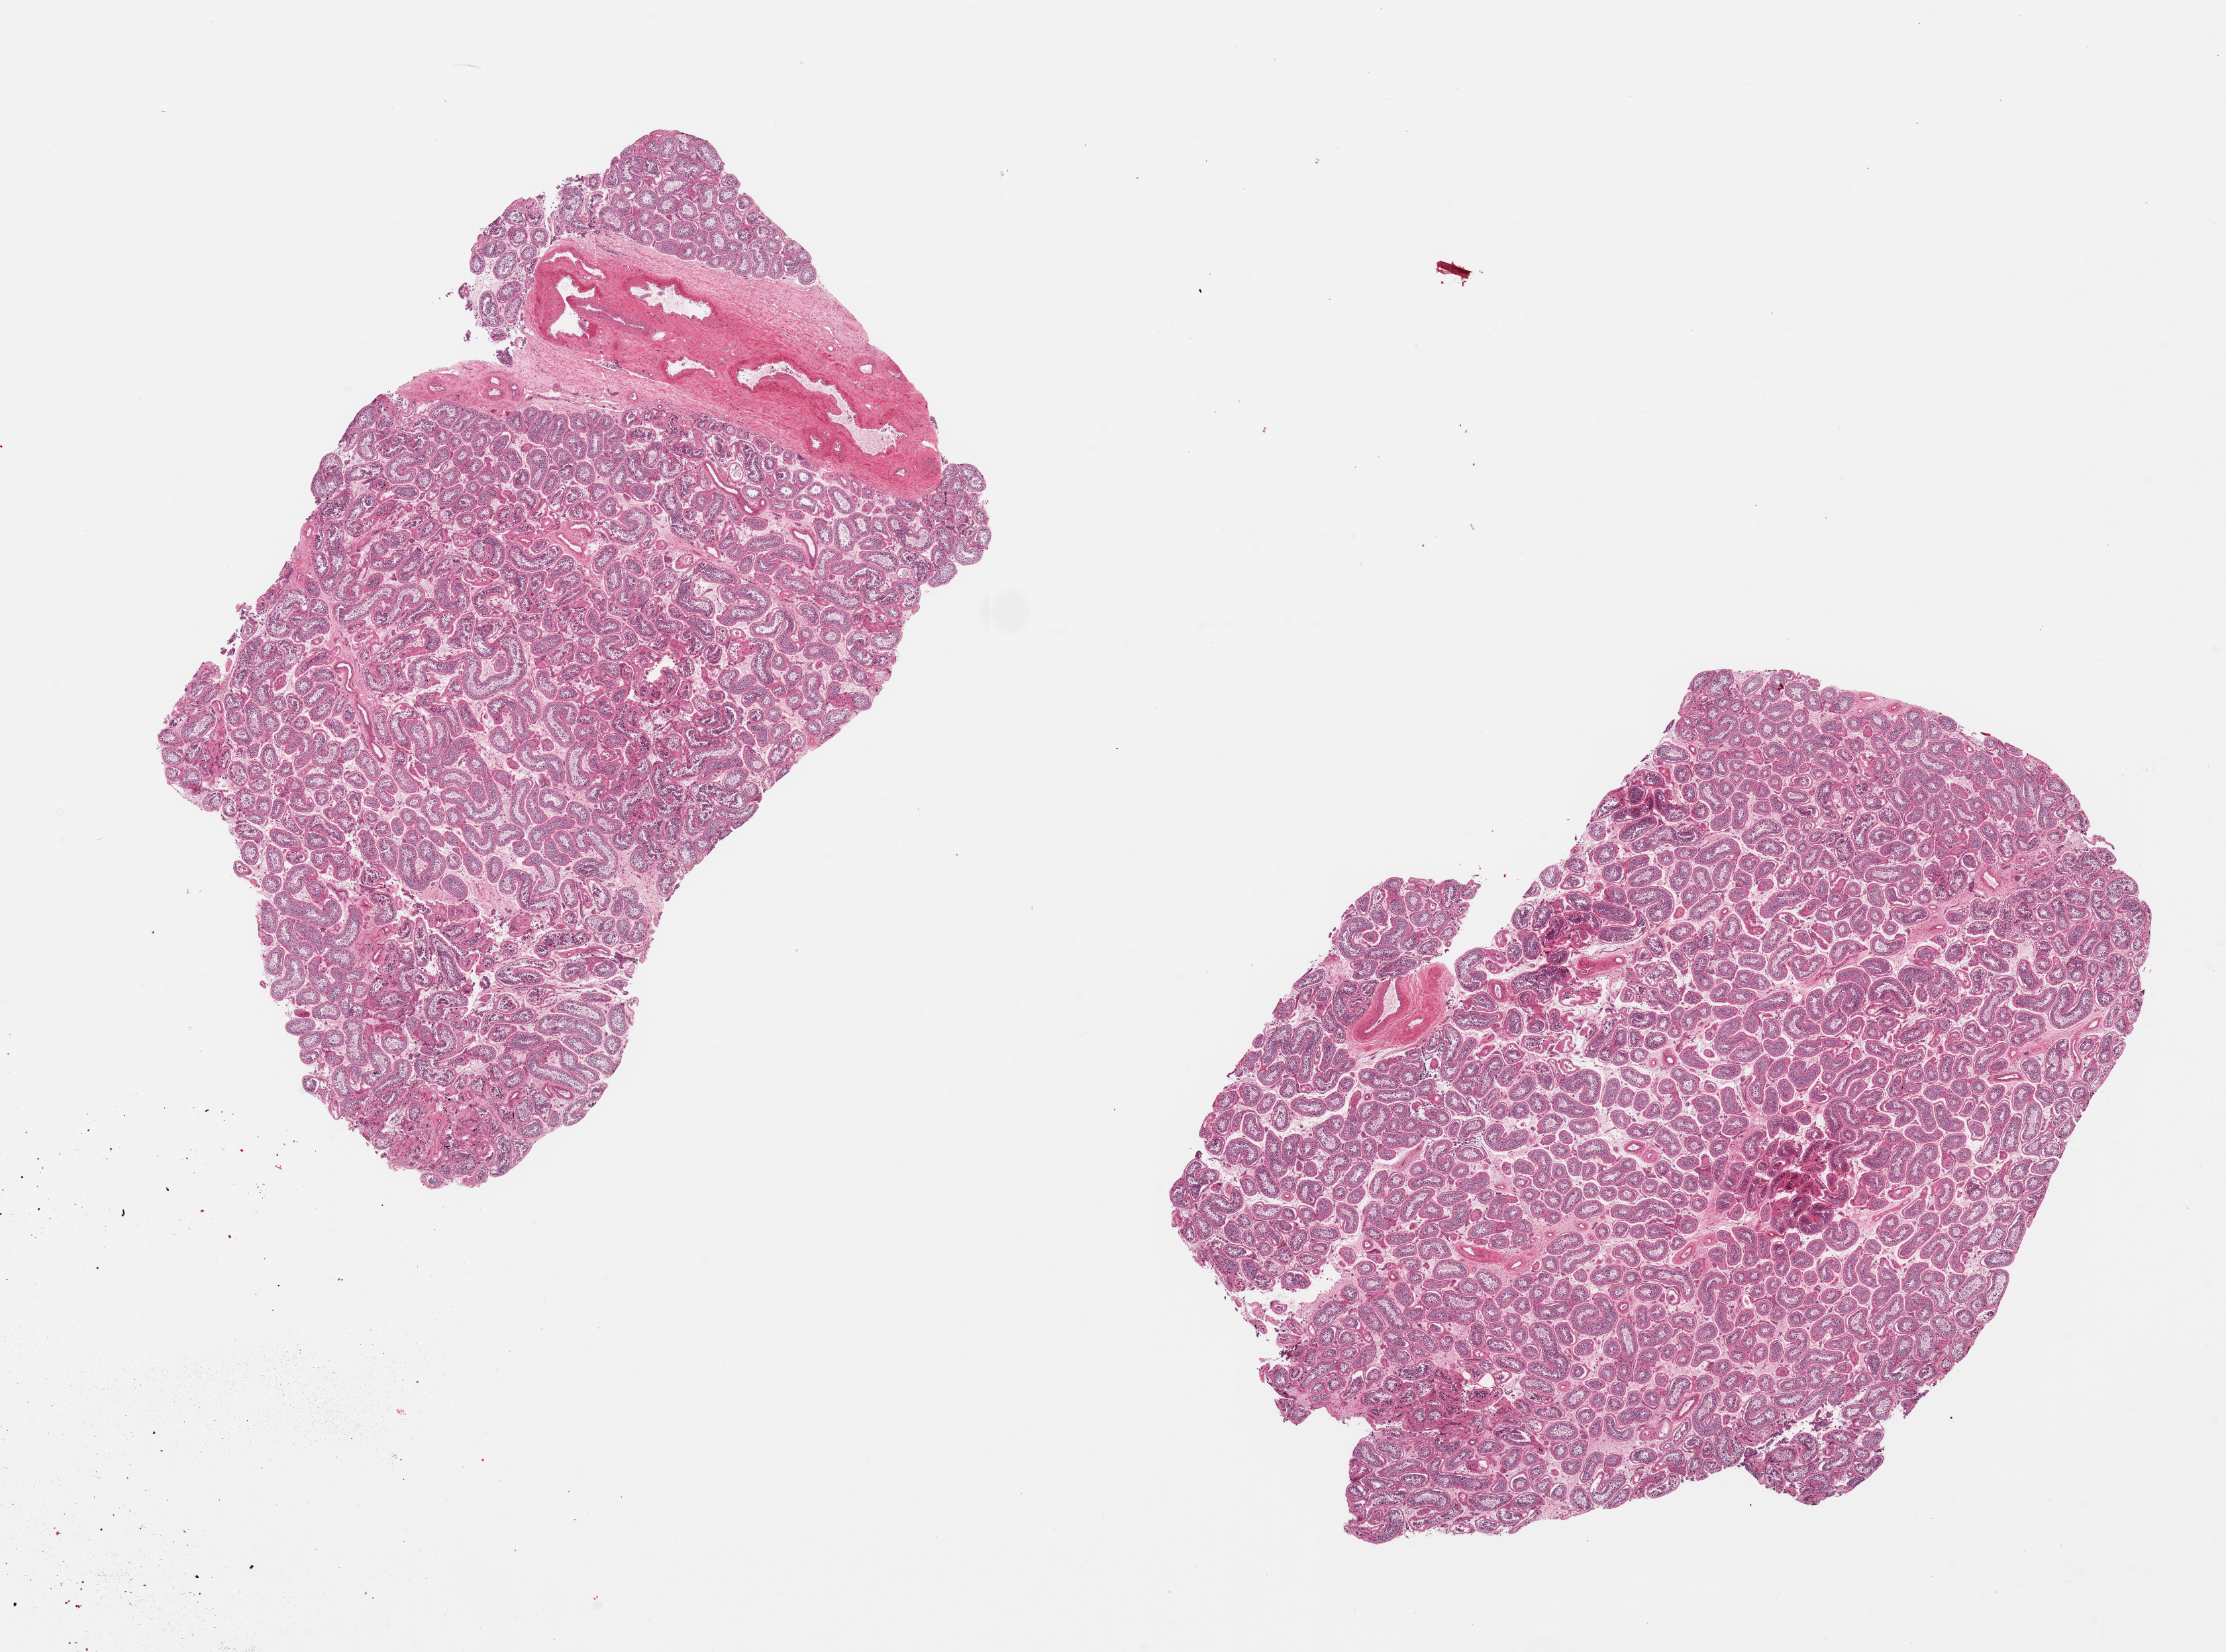
Digitized hematoxylin and eosin (H&E)-stained section, brightfield — shown as a low-resolution overview of the whole scanned area (about 26.6 x 19.7 mm, acquisition: 20x scan), PAXgene-fixed, paraffin-embedded tissue, sampled site (target tissue): testis, tissue donor sample.
Reviewer comment on this tissue sample: 2 pieces ~8x6mm. Spermatogenesis present.